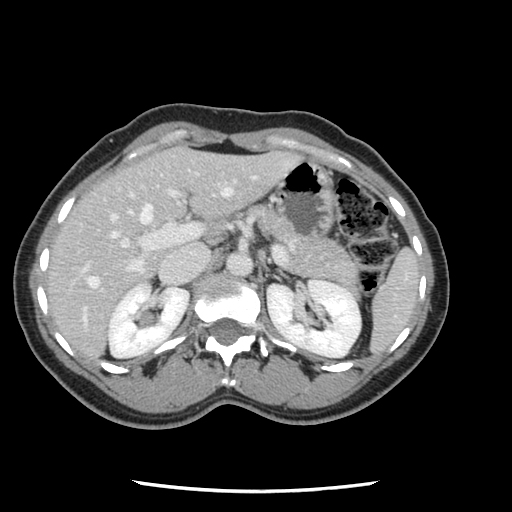
Contrast-enhanced abdominal CT, one axial slice; intravenous contrast given; soft-tissue window (W 400 / L 40 HU); 2.5 mm slice thickness; 512 × 512 image matrix, field of view 330 × 330 mm. Female patient, age 43 years. Case-level facts recorded for this patient, not image findings: diagnosis: colorectal cancer liver metastases, imaged before liver resection; multiple liver metastases: yes; largest metastasis: 3.4 cm; chemotherapy before resection: no.
Structures marked on this image (outlined manually by an expert reader):
- hepatic veins: bounding box <83,188,231,322> (left, top, right, bottom; pixels)
- liver: <47,147,295,359>
- planned liver remnant (the part of the liver to remain after resection): <47,150,186,303>
- portal vein (with intrahepatic branches): <70,181,235,290>